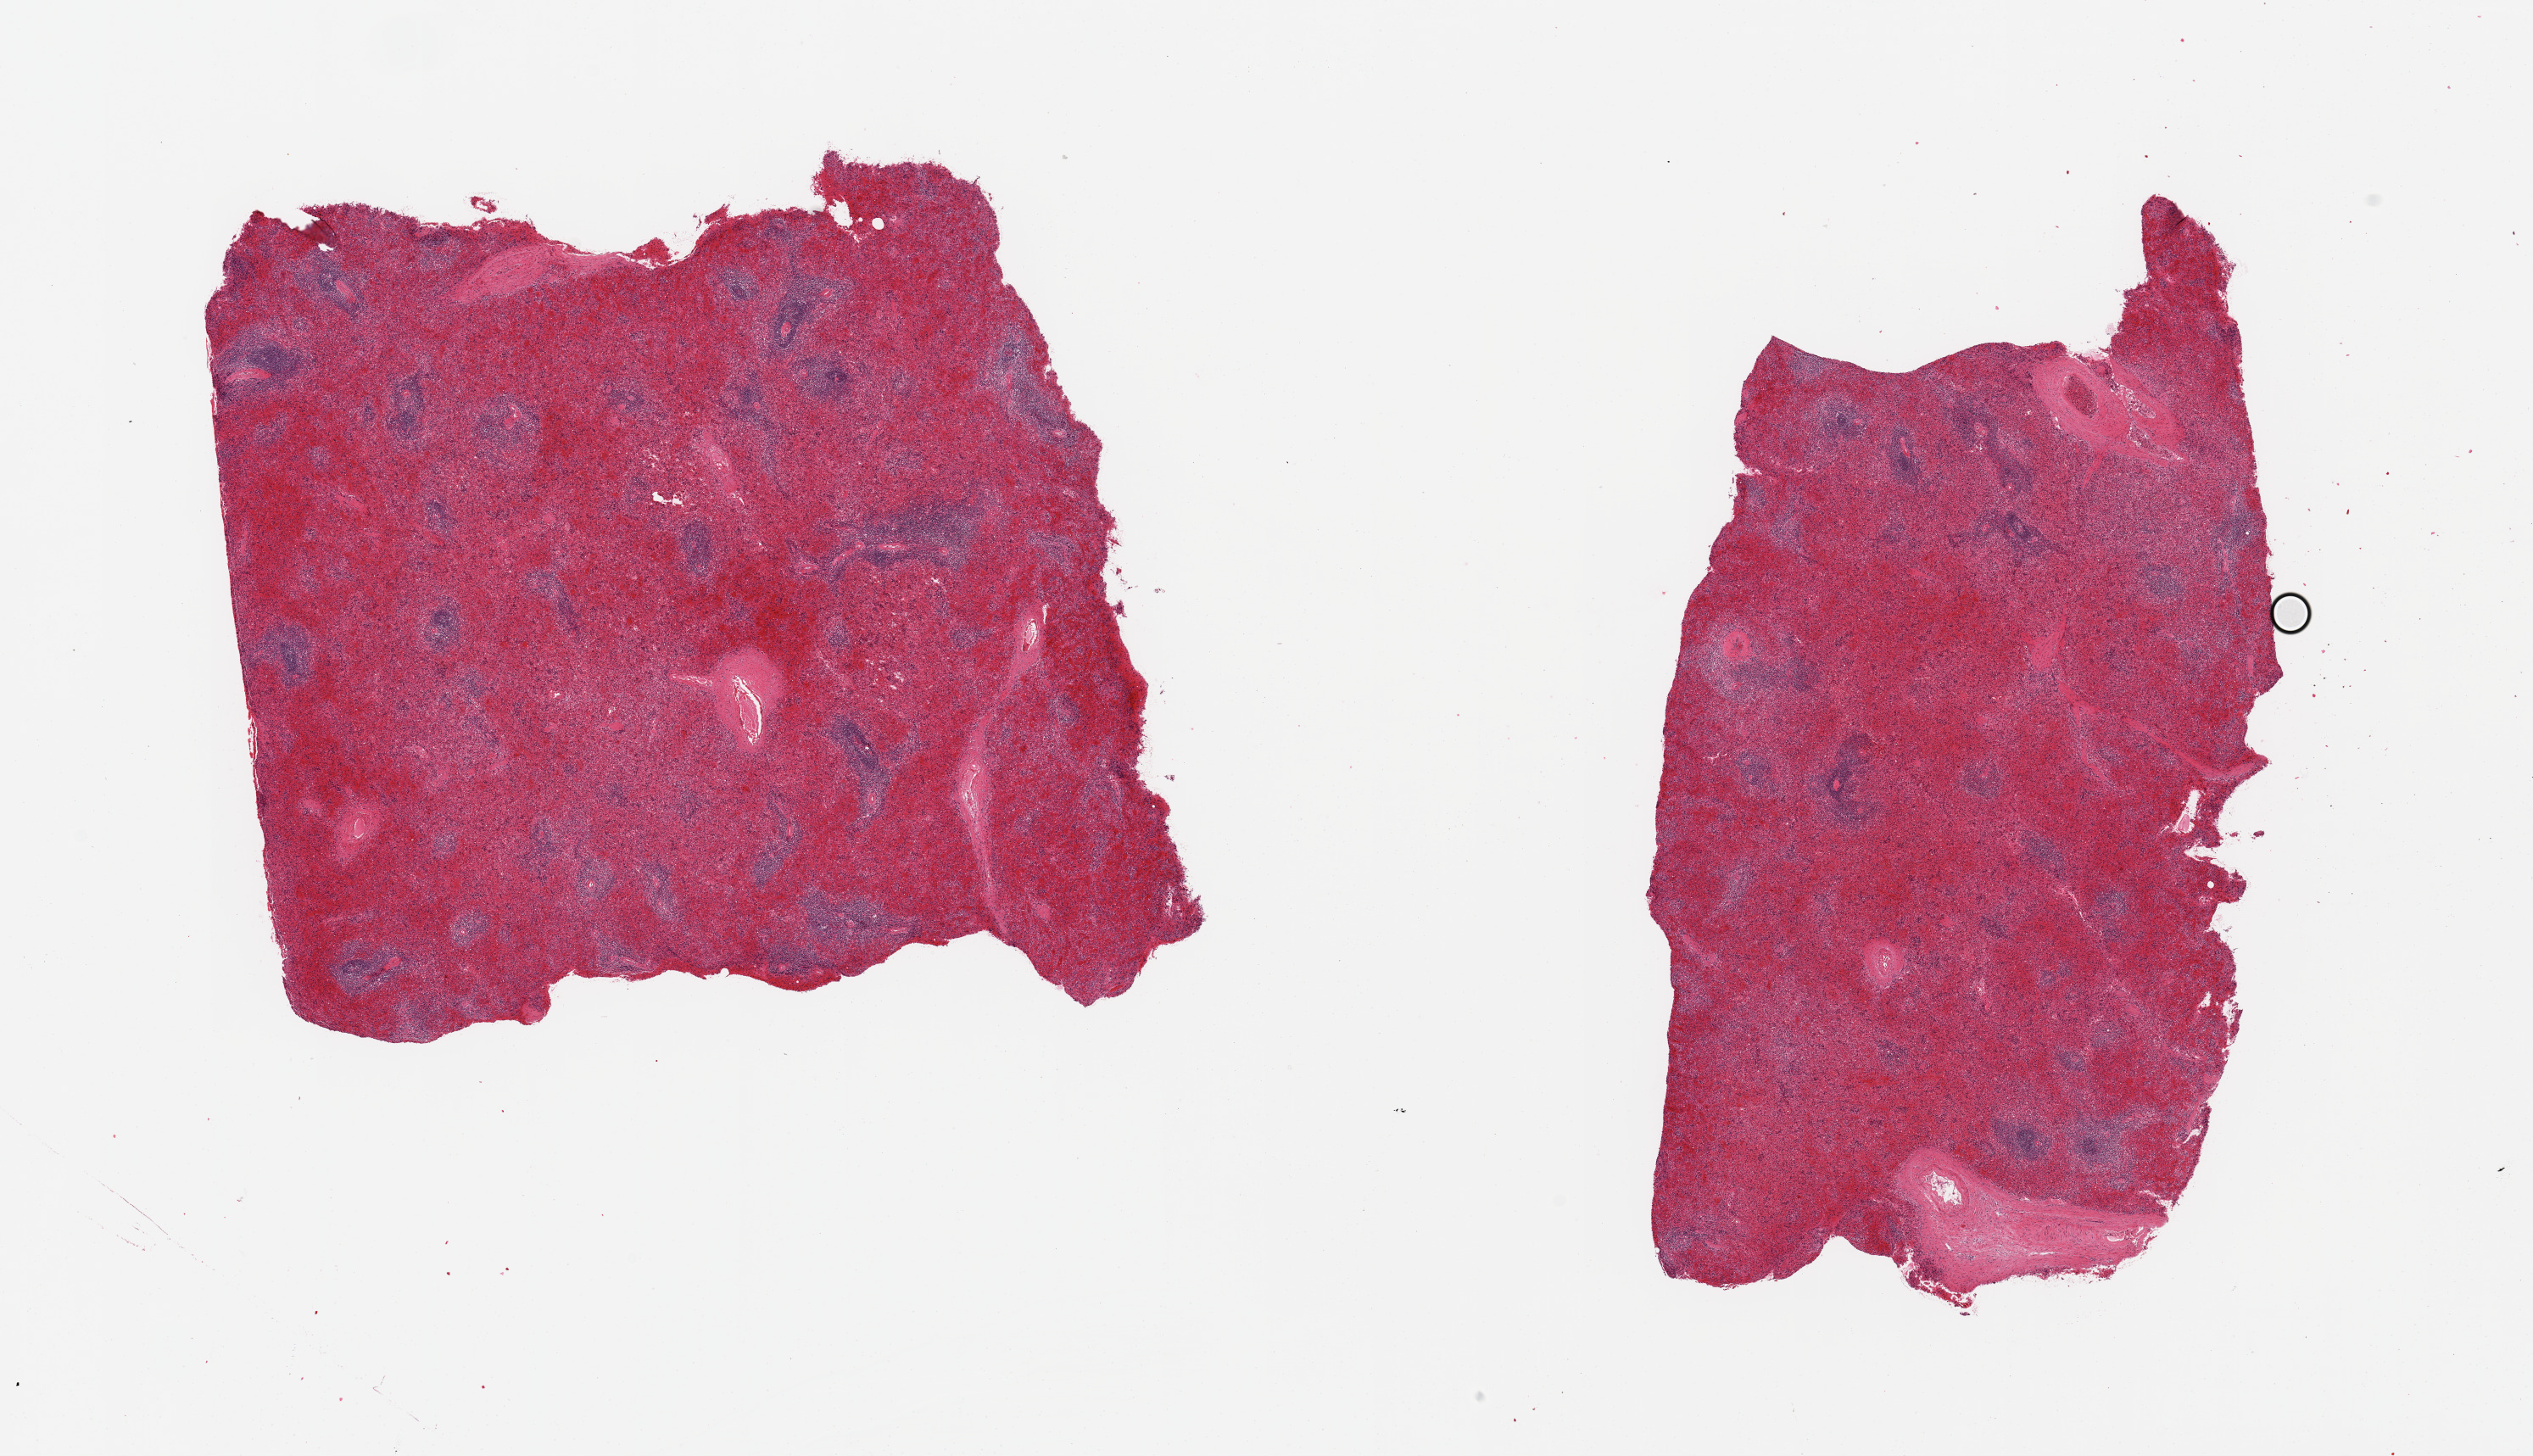
Digitized haematoxylin and eosin-stained section, low-resolution overview of the scanned area, about 23.6 x 13.6 mm (acquisition: 20x scan); PAXgene-fixed paraffin-embedded (PFPE) section; sampled site (target tissue): spleen; donor tissue sample. Female donor.
Pathologist's review note for this sample: 2 pieces; congested.